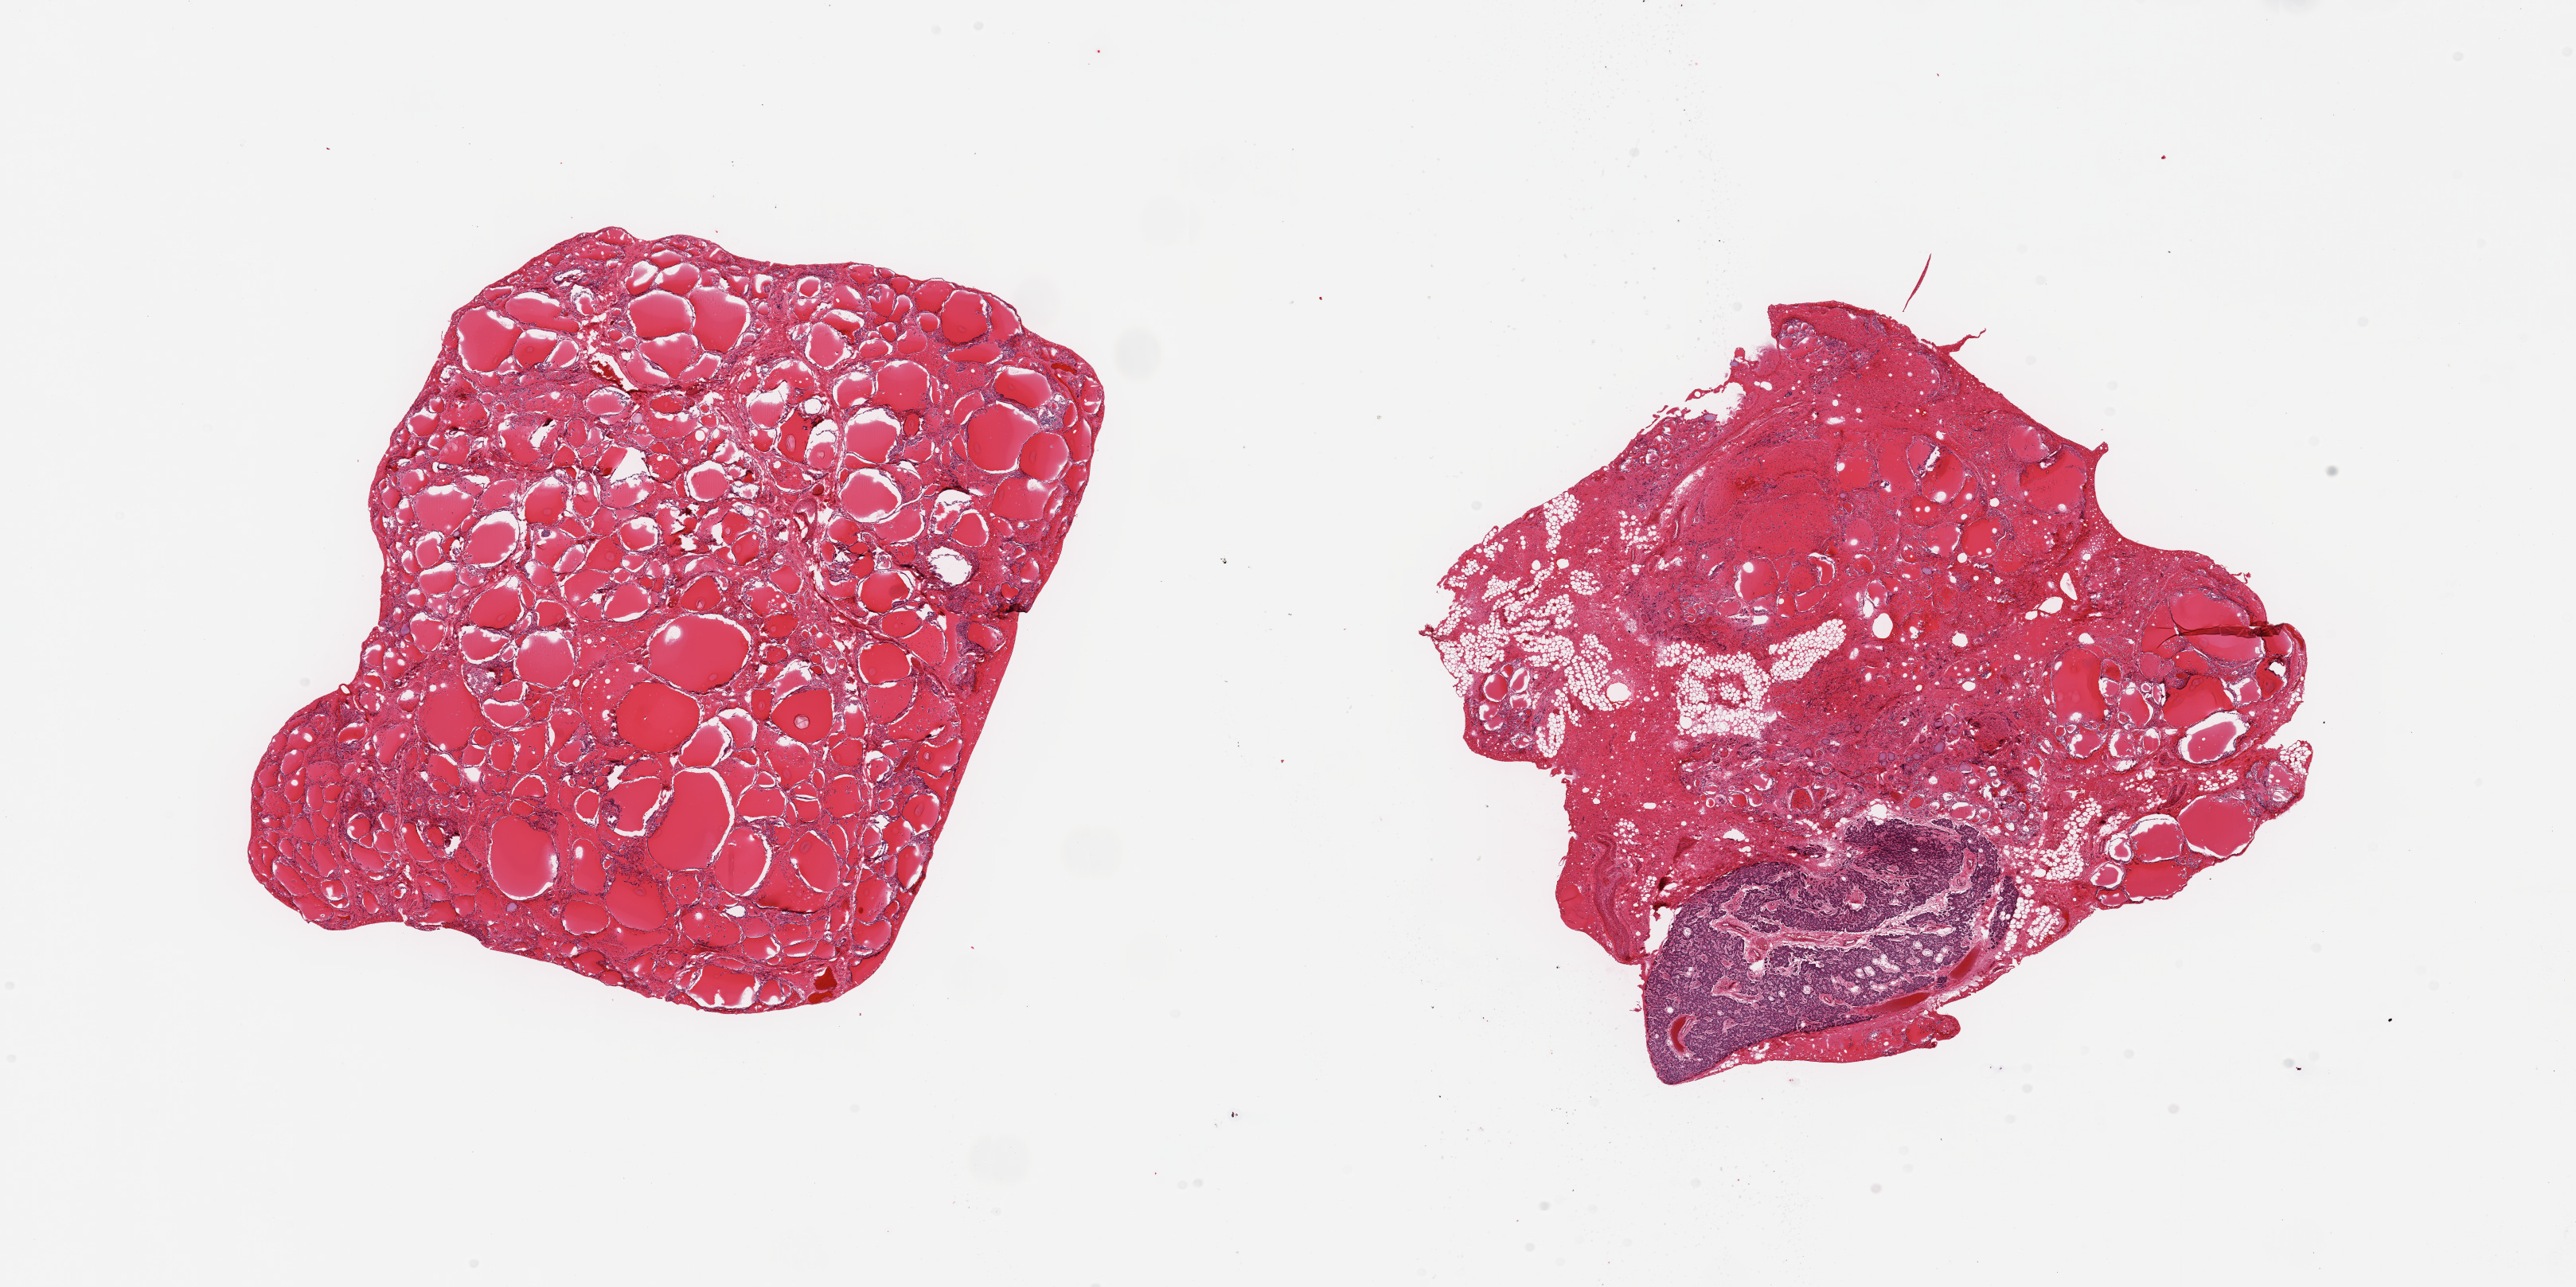
Digitized H&E-stained section — shown as a low-resolution overview of the whole scanned area (about 25.6 x 12.8 mm), PAXgene-fixed paraffin-embedded (PFPE) section, target tissue: thyroid, tissue donor sample. Donor: male.
* pathologist's review note for this sample: 2 pieces; 1 piece is entirely thyroid, second includes 4mm parathyroid and surrounding stroma and fat/~50% thyroid, nodular goiter